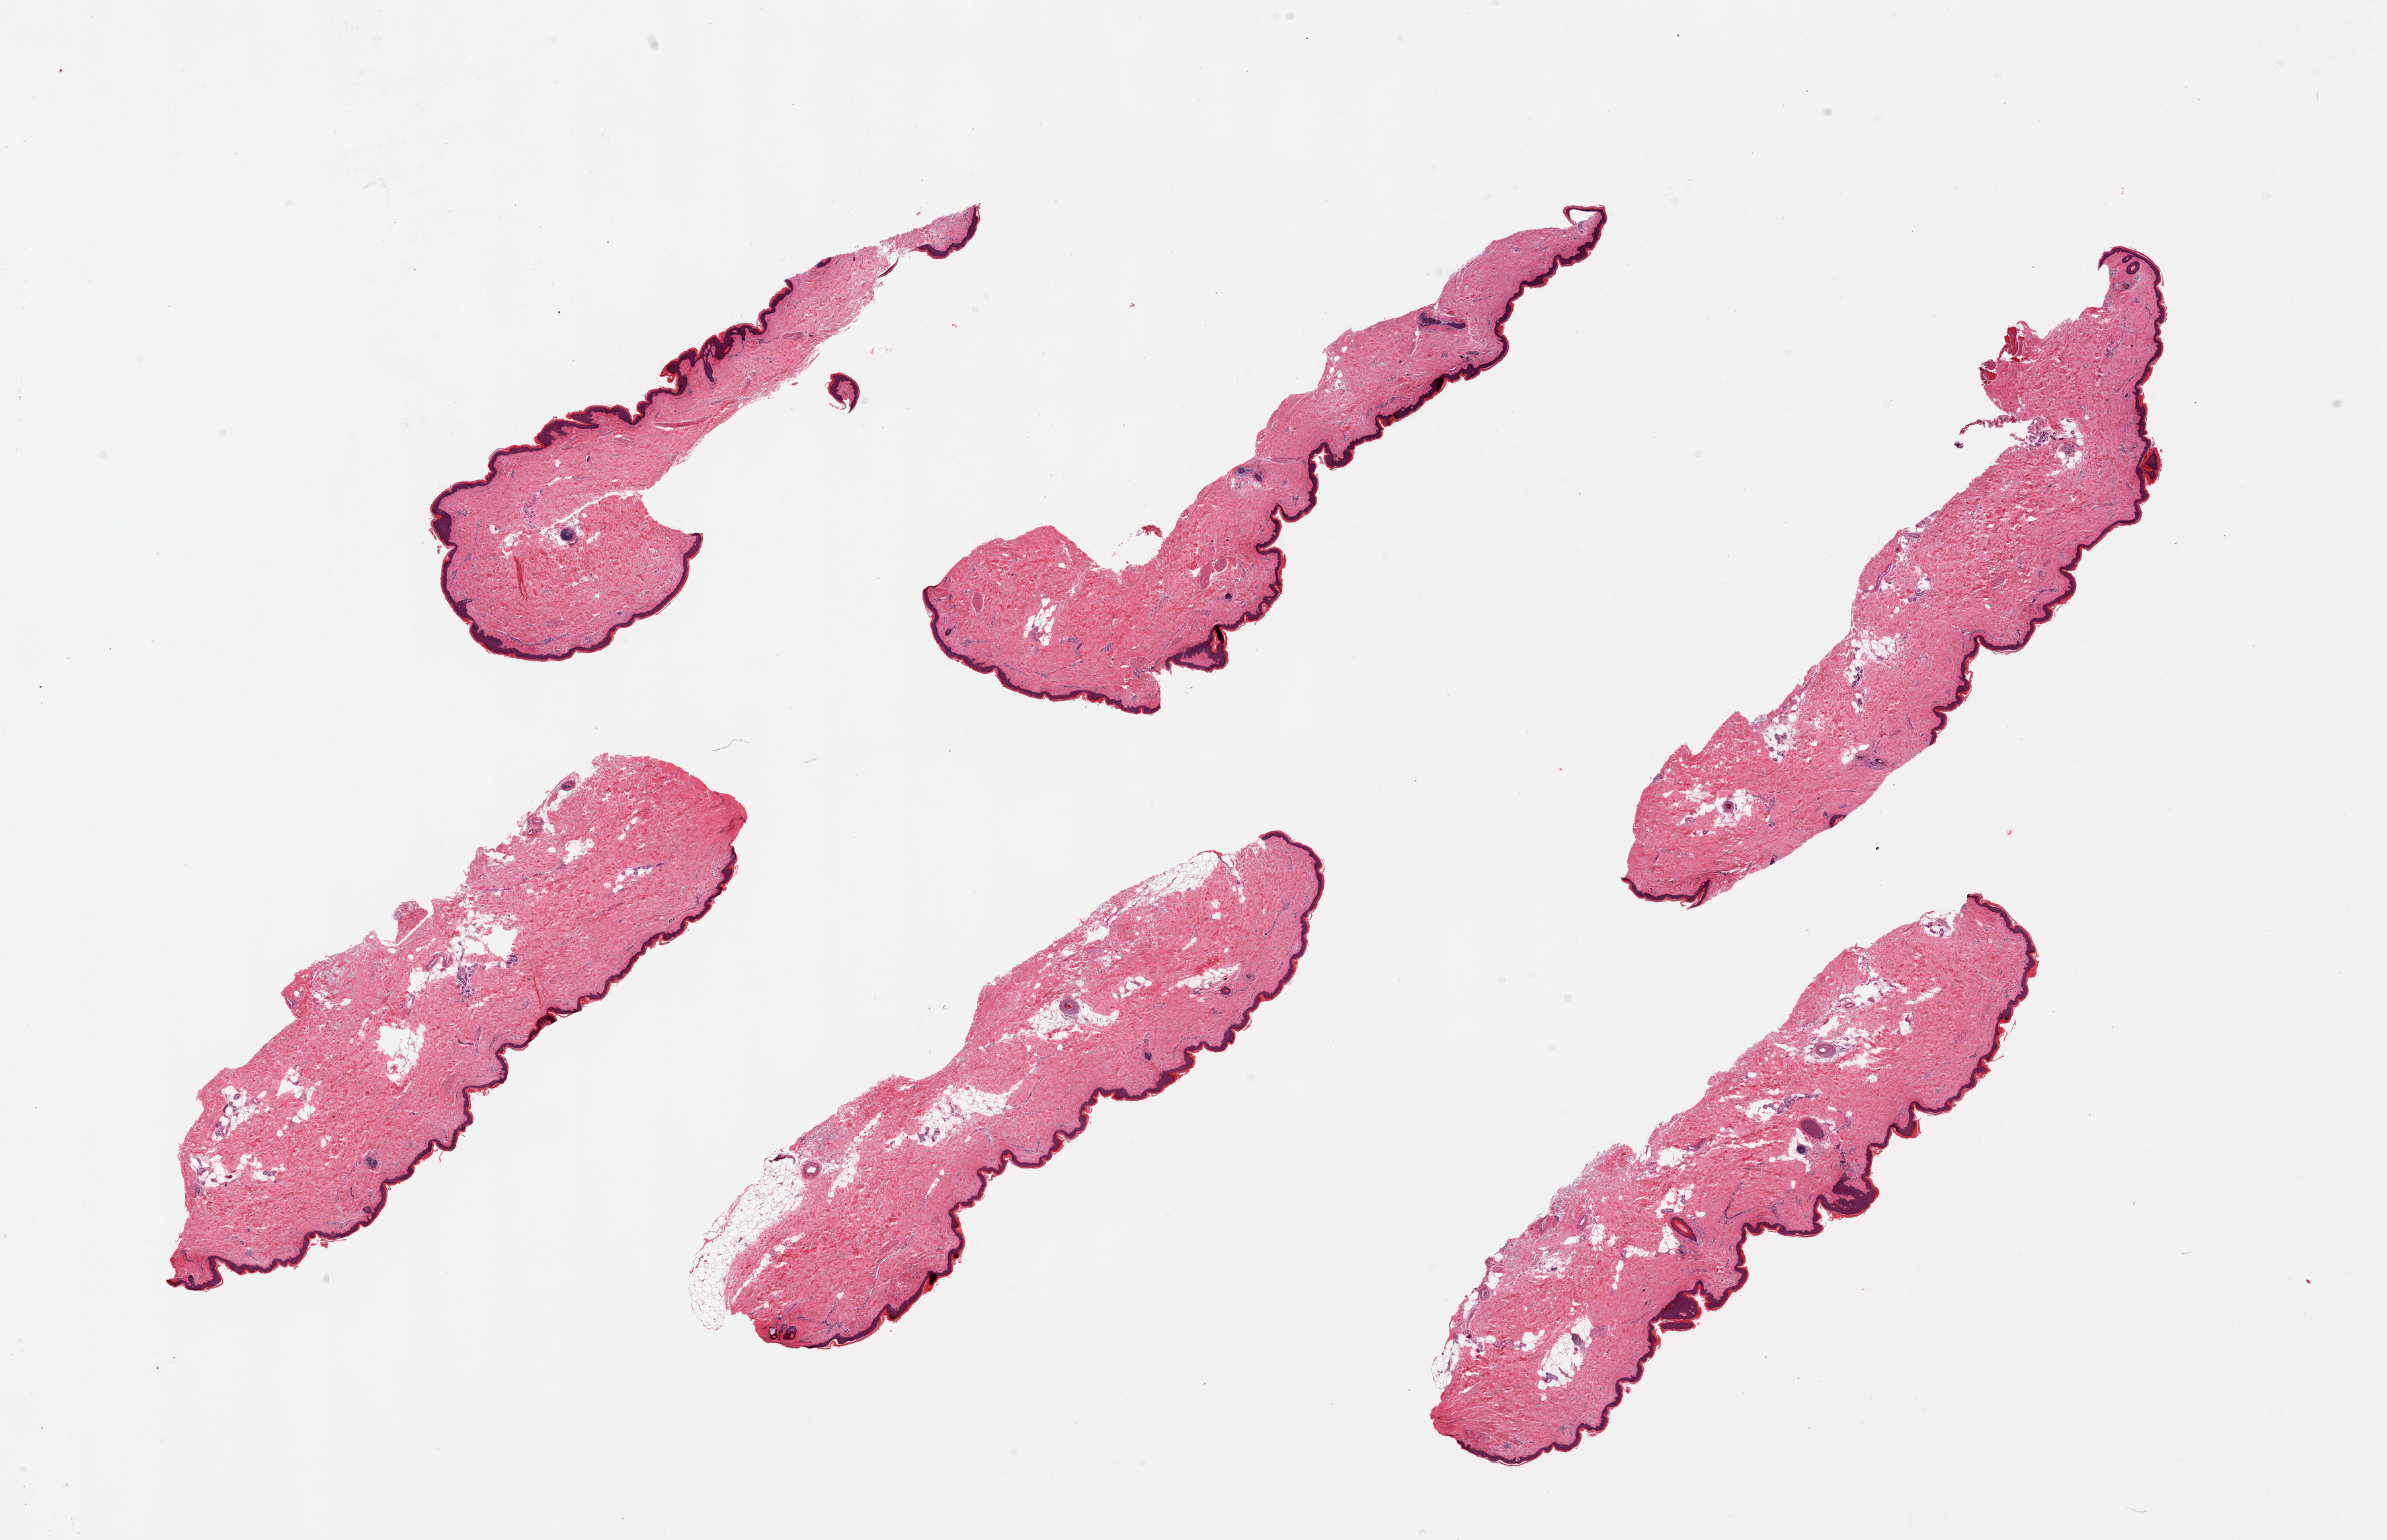
Whole-slide image, haematoxylin and eosin stain, a low-resolution overview of the entire scanned area, about 28.5 x 18.4 mm; PAXgene-fixed, paraffin-embedded tissue; section of skin of lower leg (target tissue); donor tissue sample. Donor sex: female.
Reviewer comment on this tissue sample: 6 pieces; mostly well trimmed with up to 10% fat (predominantly internal), epidermis measures 52 microns, detached fragment of skeletal muscle.